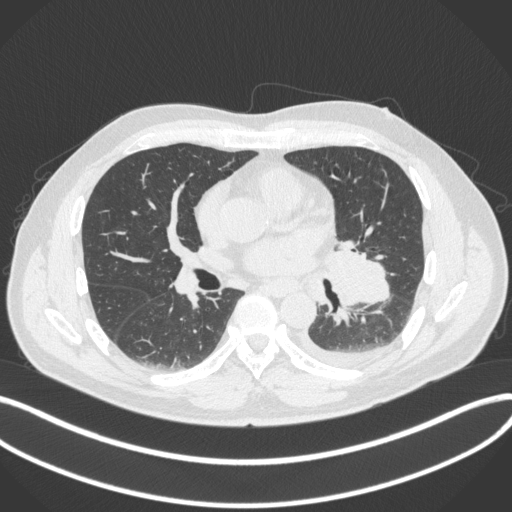
Chest CT, one axial slice. Slice 186 of 350 in the series (ordered by position). 120 kVp. Lung window (W 1500 / L -600 HU). 512 × 512 image matrix, field of view 400 × 400 mm. Male patient, age 58 years. Case-level facts recorded for this patient, not image findings: clinical TNM (as recorded): T3 N1 M1b.
Annotated regions visible in this slice (bounding box drawn by a radiologist):
- lung tumour (recorded histology: small cell carcinoma): bounding box (x1, y1, x2, y2) in pixels: (315, 240, 394, 317)